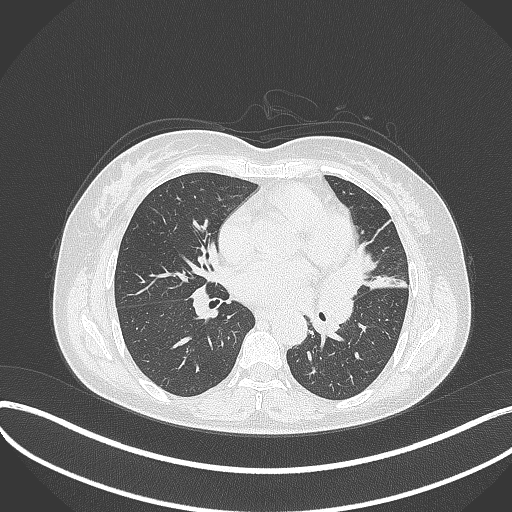
Chest CT, one axial slice. Lung window (W 1500 / L -600 HU). 1 mm slice thickness. 512 × 512 image matrix, field of view 400 × 400 mm. Patient: female, 54 years. Case-level facts recorded for this patient, not image findings: clinical TNM (as recorded): T2a N1 M0; histopathological grade: G3.
Annotated regions visible in this slice (rectangle marked by the reading radiologist):
- lung tumour (recorded histology: small cell carcinoma): bounding box <316,255,380,328> (left, top, right, bottom; pixels)